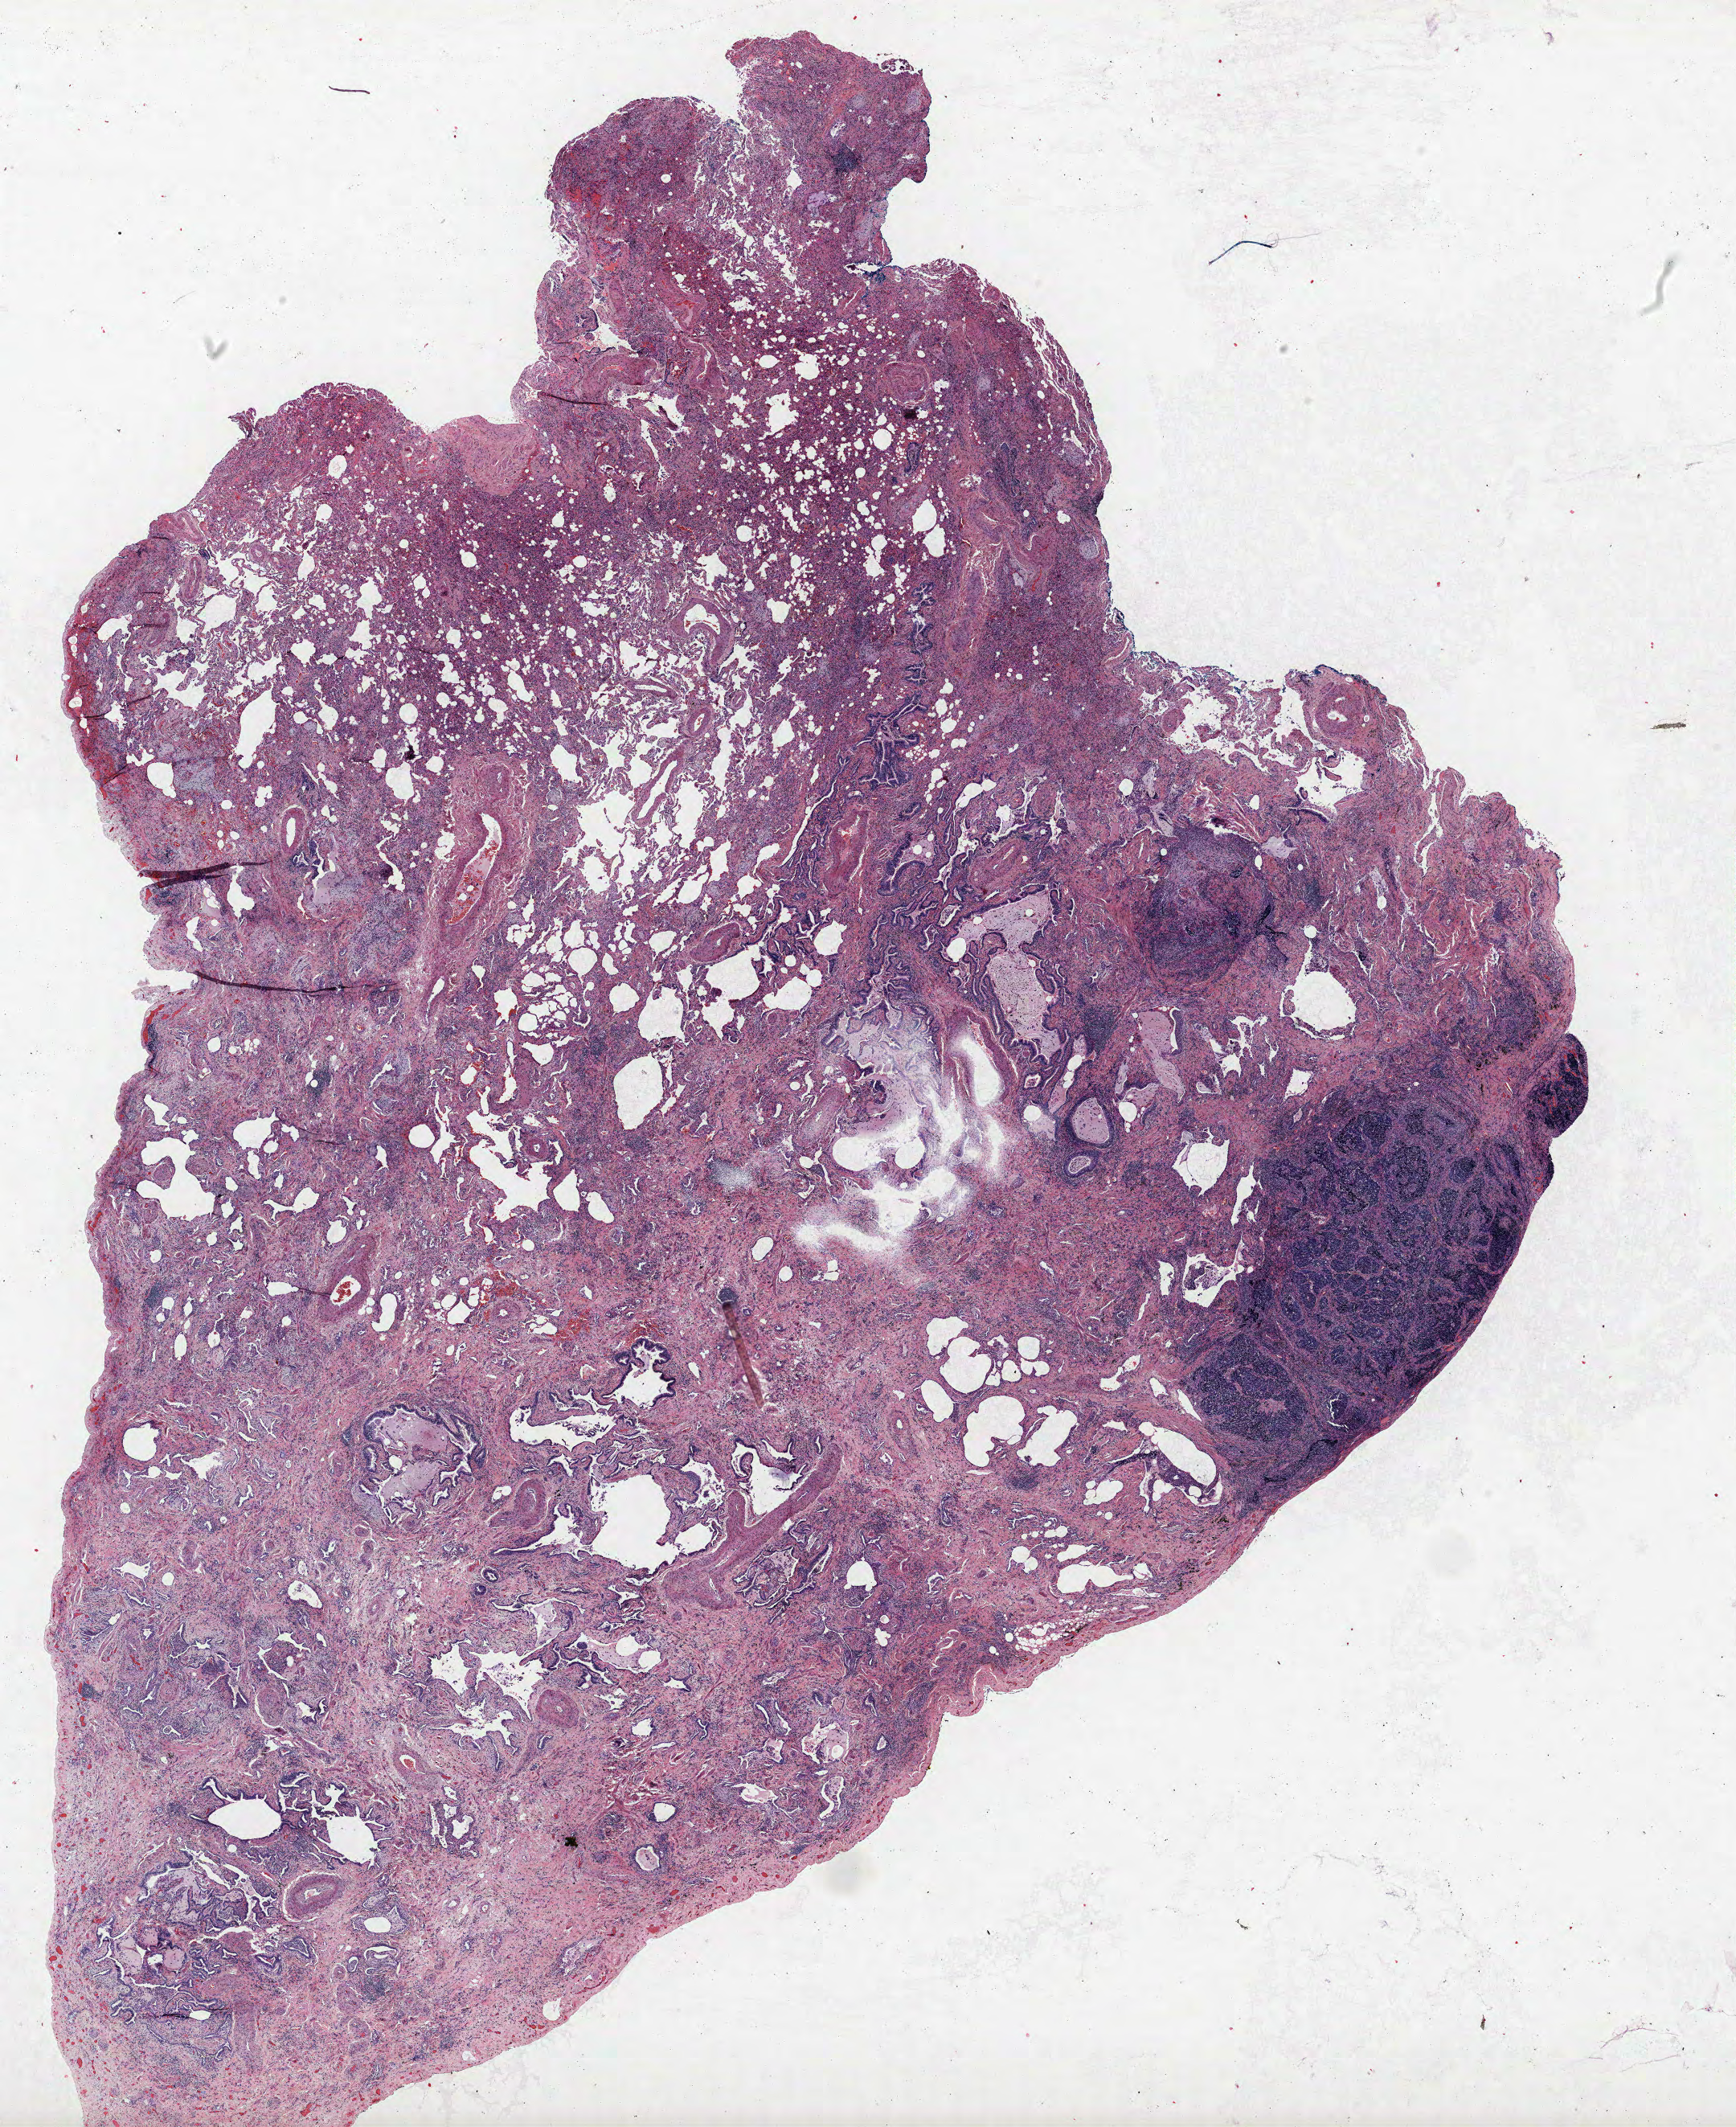
H&E-stained whole-slide image — shown as a low-resolution overview of the whole scanned area (about 17.3 x 21.2 mm, acquisition: 40x scan). Formalin-fixed paraffin-embedded (FFPE) section. Lung. Male, age 56 at enrolment.
Participant's lung-cancer diagnosis: Large cell neuroendocrine carcinoma.